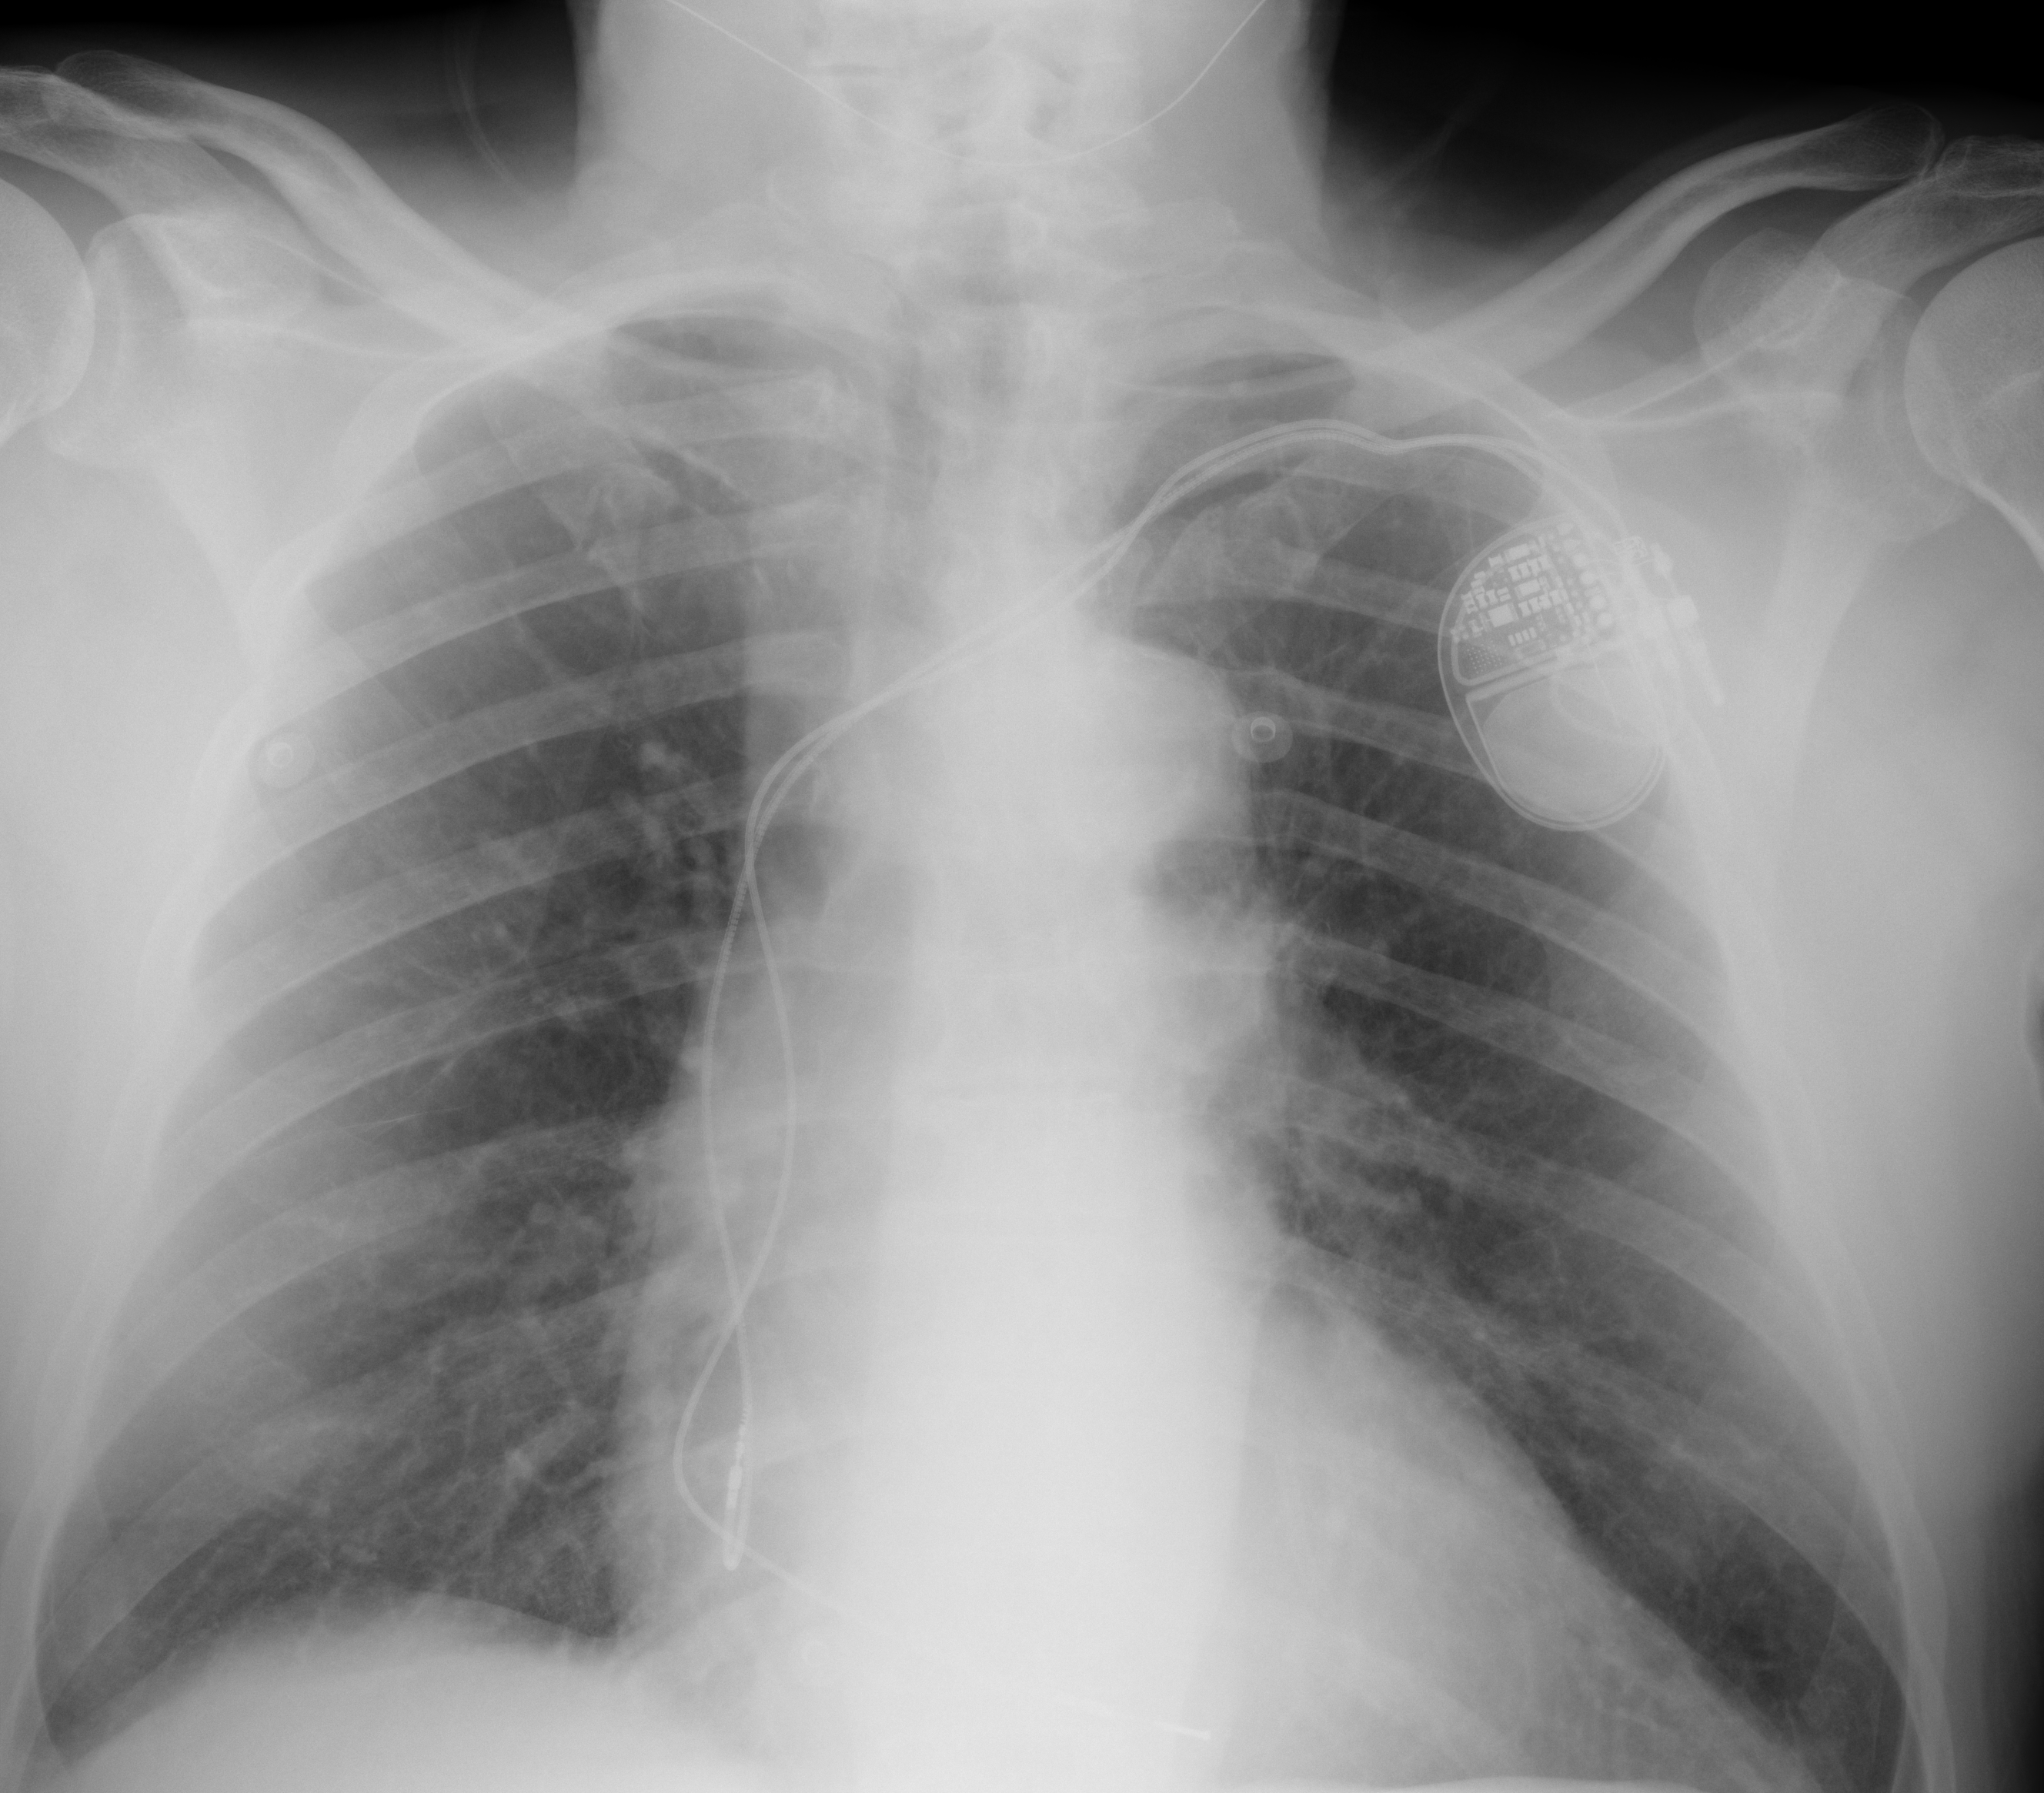
Chest X-ray (portable), AP projection. Male patient, age 79 years; imaged 0 days after the COVID-19 diagnosis.
Radiologist key findings (as recorded): No significant airspace consolidation evident bilaterally.